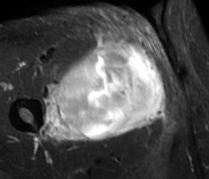
MRI of an extremity soft-tissue mass, one axial slice. Position 43 of 89 along the scan axis. STIR. MR volume resampled by the dataset authors to the PET/CT grid (not the native acquisition matrix). 3.27 mm slice thickness. 209 × 179 image matrix. Male patient. From the clinical record (not read from this slice): histological type: undifferentiated - pleiomorphic; grade: high; site of the primary tumour: right thigh.
Outlined on this slice (expert contour drawn on MRI and transferred to this co-registered scan by the dataset authors):
- gross tumour volume including surrounding oedema: bounding box <41,39,166,143> (left, top, right, bottom; pixels)
- gross tumour volume (mass): <55,41,165,138>